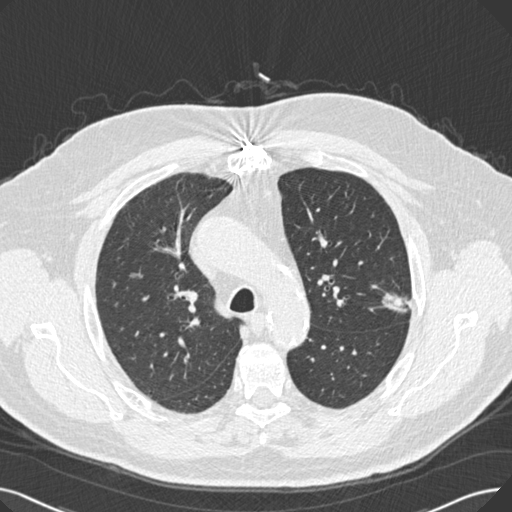
Low-dose screening chest CT, one axial slice; slice 187 of 269 in the series (ordered by position); reconstruction kernel B30f; 120 kVp; lung window (W 1500 / L -600 HU); 512 × 512 image matrix, field of view 370 × 370 mm.
Annotated regions visible in this slice (expert manual segmentation):
- lesion 1 (tumor, upper lobe of left lung): bounding box <382,293,410,313> (left, top, right, bottom; pixels)